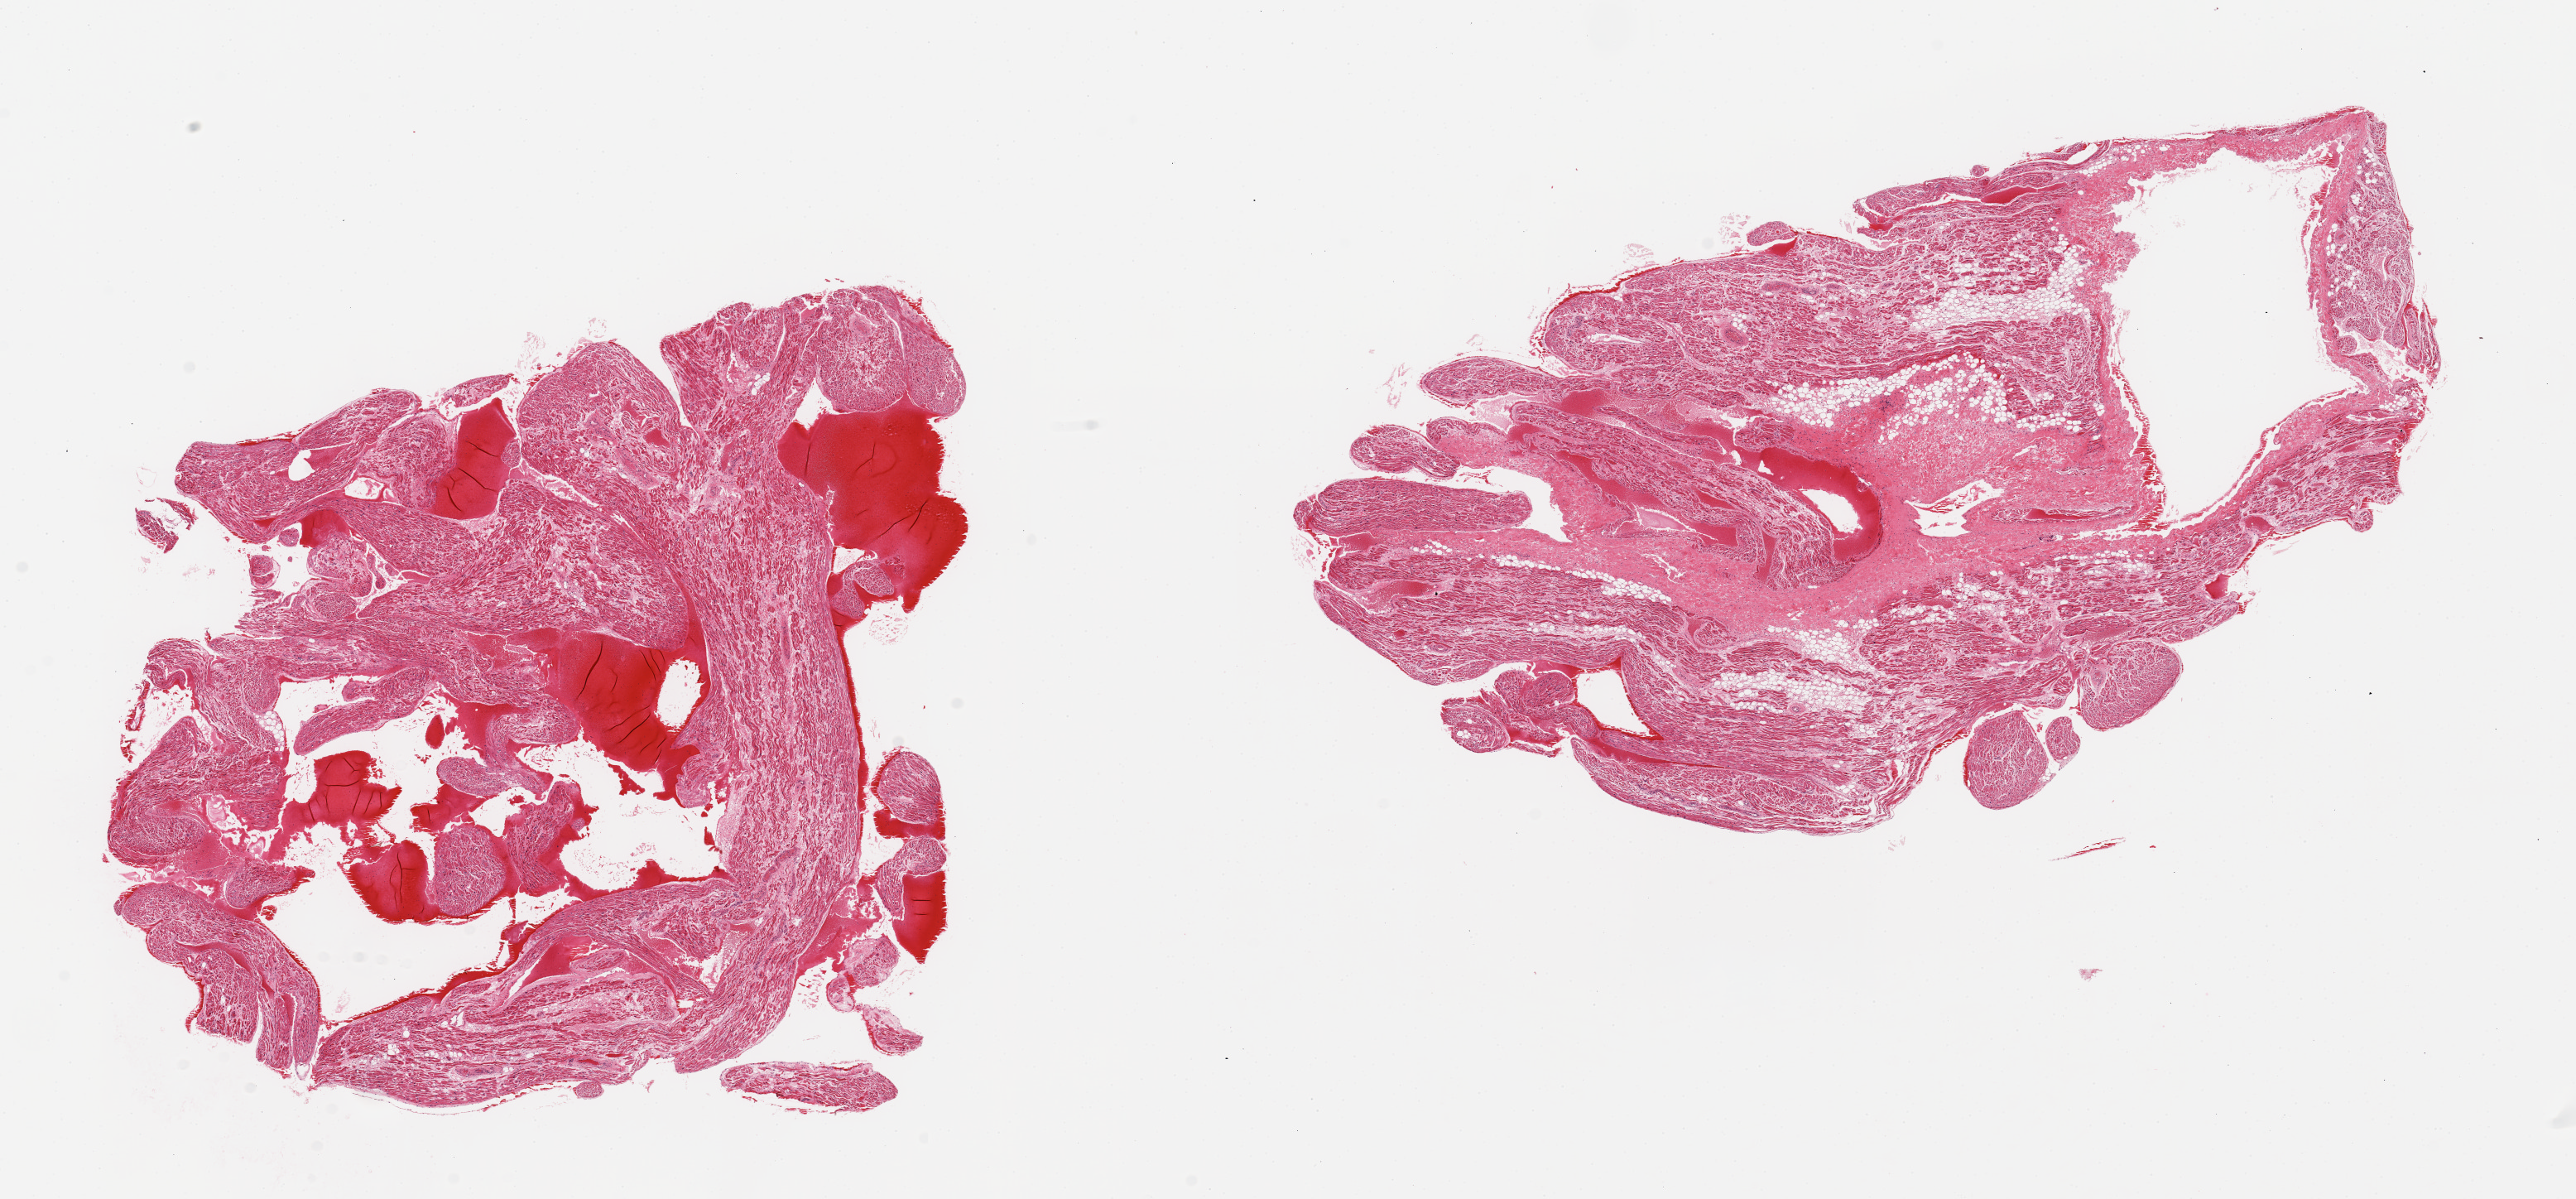
Digitized H&E-stained section, brightfield, shown as a low-resolution overview of the whole scanned area (about 24.6 x 11.5 mm, from a 20x scan), PAXgene-fixed, paraffin-embedded tissue, section of auricular appendage (target tissue), tissue donor sample. Donor sex: female.
Review note (as recorded): 2 pieces; one with 20% internal fat and fibrous tissue.